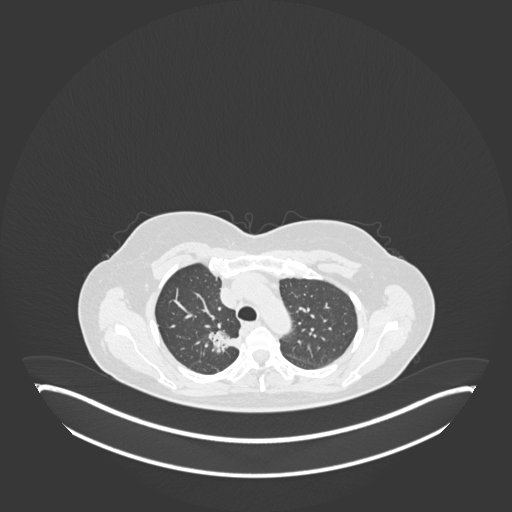
Chest CT, one axial slice. Slice 134 of 181 in the series (ordered by position). Lung window (W 1500 / L -600 HU). 512 × 512 image matrix. Patient: female, 65 years. Case-level facts recorded for this patient, not image findings: clinical TNM (as recorded): T1b N0 M0; histopathological grade: G2.
Annotated regions visible in this slice (rectangle marked by the reading radiologist):
- lung tumour (recorded histology: adenocarcinoma): box from (x=205, y=326) to (x=242, y=355) px